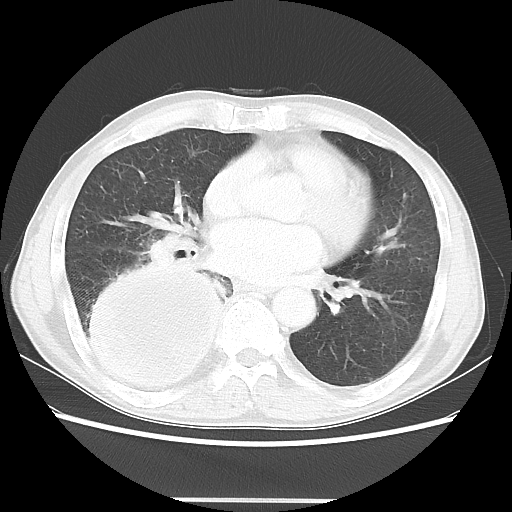
Chest CT, one axial slice. Slice 20 of 48 in the series (ordered by position). Reconstruction kernel LUNG. 100 kVp. Lung window (W 1500 / L -600 HU). 5 mm slice thickness. 512 × 512 image matrix, field of view 361 × 361 mm. Patient: male, 66 years. Case-level facts recorded for this patient, not image findings: clinical TNM (as recorded): T4 N1 M1; histopathological grade: G3.
Outlined on this slice (bounding box drawn by a radiologist):
- lung tumour (recorded histology: small cell carcinoma): bounding box [x1, y1, x2, y2] px = [76, 259, 232, 396]